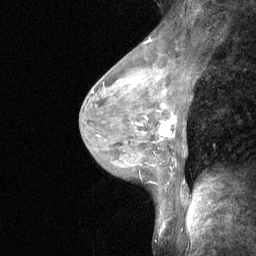
Breast MRI (dynamic contrast-enhanced), one sagittal slice; position 36 of 64 along the scan axis; dynamic contrast-enhanced study with each time point stored as its own series, time point 2 of 3 at this slice position (early post-contrast, ordered by acquisition time); 1.5 T; TE 4.8 ms, TR 27 ms; 2 mm slice thickness; 256 × 256 image matrix, field of view 200 × 200 mm. Patient: female, 44 years. Case-level facts recorded for this patient, not image findings: setting: breast cancer imaged before/during neoadjuvant chemotherapy; receptor status: HR-positive, HER2-negative.
Outlined on this slice (semi-automatic segmentation, software-assisted and operator-edited):
- analysis volume of interest (the breast-tissue region the enhancement analysis was run in; not a lesion): bounding box <140,109,180,148> (left, top, right, bottom; pixels)
- tumour enhancement mask (voxels above the 90 % enhancement threshold inside the analysis volume of interest): <159,117,176,137>